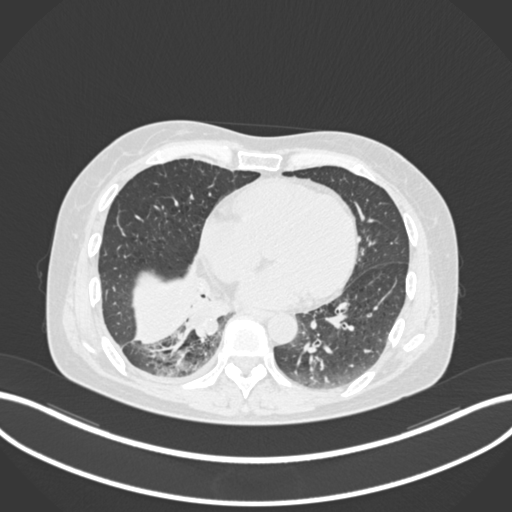
Chest CT, one axial slice; position 56 of 168 along the scan axis; reconstruction kernel B30f; lung window (W 1500 / L -600 HU); 1 mm slice thickness; 512 × 512 image matrix. Patient: female, 63 years. From the clinical record (not read from this slice): clinical TNM (as recorded): T1c N0 M0.
Annotated regions visible in this slice (rectangle marked by the reading radiologist):
- lung tumour (recorded histology: adenocarcinoma): box from (x=181, y=295) to (x=240, y=339) px